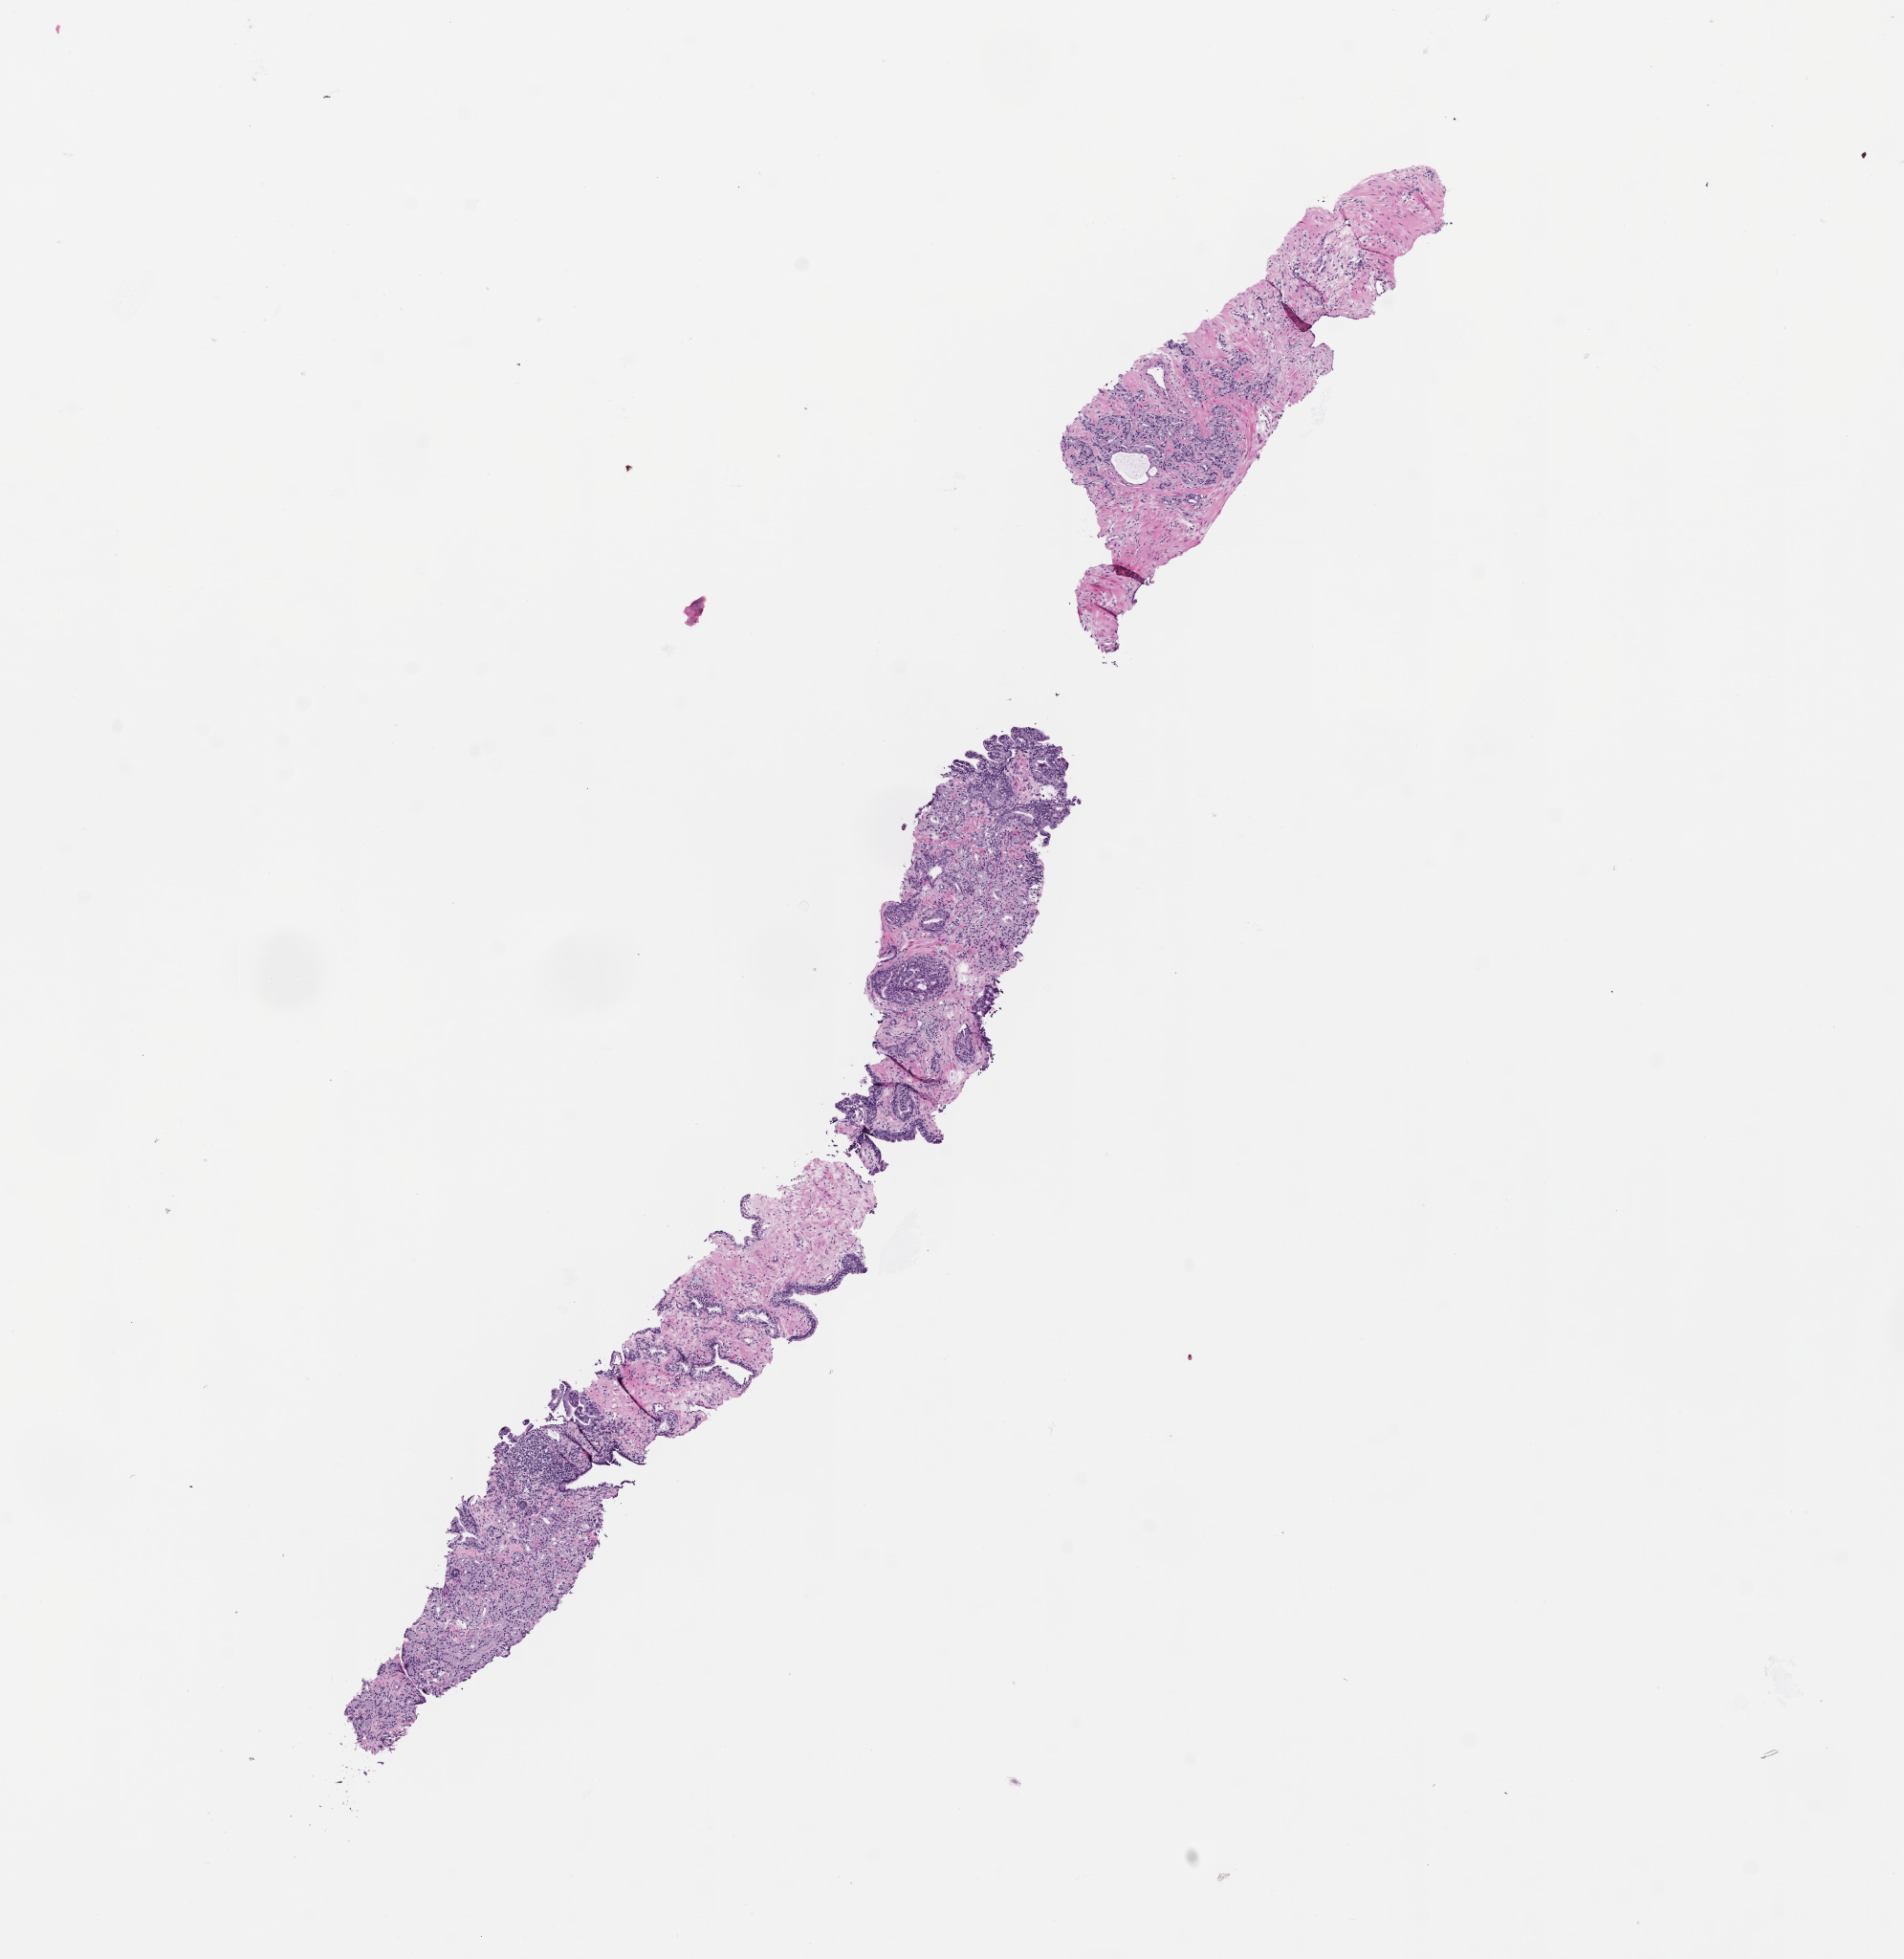
Hematoxylin and eosin (H&E) whole-slide image, whole scanned area (about 8.0 x 8.3 mm) shown as a low-resolution overview; formalin-fixed, paraffin-embedded (FFPE) tissue; tissue site: prostate; archival tissue. Patient sex: male.
* this section: primary tumour tissue
* diagnosis: Prostate Carcinoma